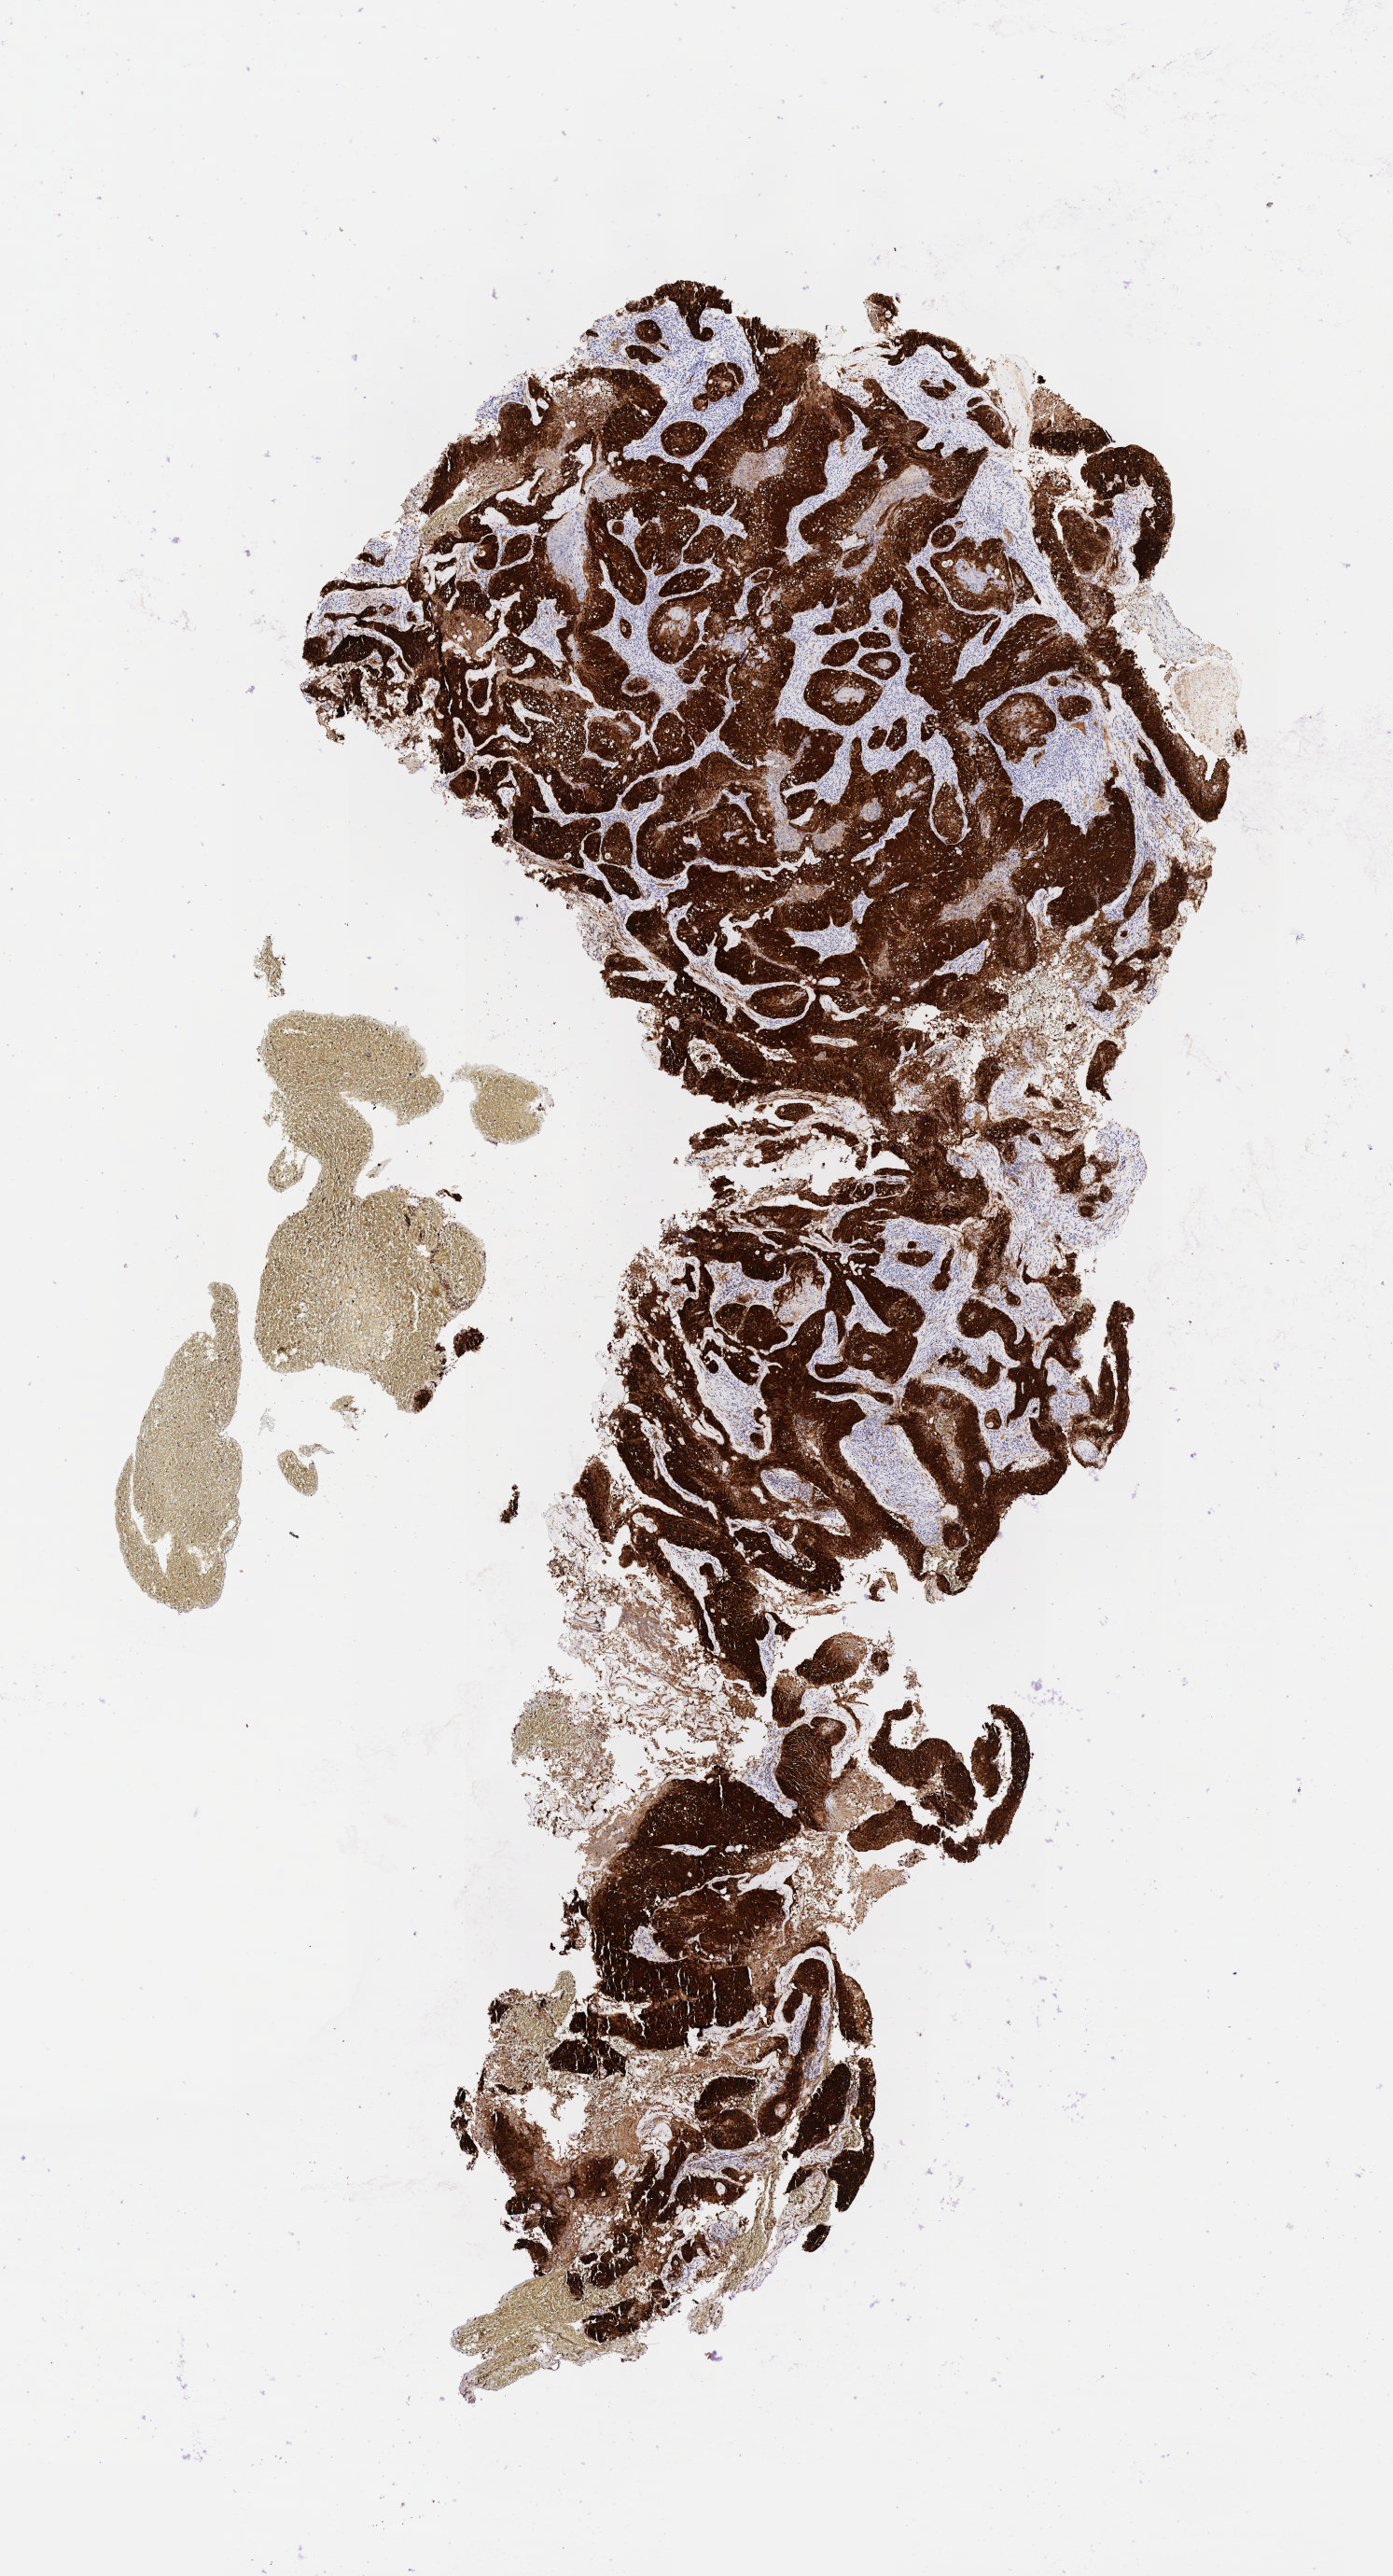
Whole-slide image, immunohistochemical stain for p16 (p16INK4a), shown as a low-resolution overview of the whole scanned area (about 6.0 x 11.2 mm). Specimen: tumor tissue. Site: cervix. Patient: female, 53 years old.
Histologic diagnosis: Squamous cell carcinoma, keratinizing, NOS.